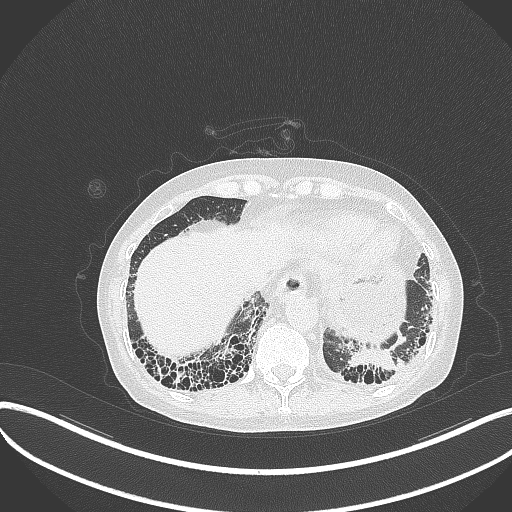
Chest CT, one axial slice. Position 58 of 373 along the scan axis. 120 kVp. Lung window (W 1500 / L -600 HU). 1 mm slice thickness. 512 × 512 image matrix, field of view 400 × 400 mm. Female patient, age 56 years. Case-level facts recorded for this patient, not image findings: clinical TNM (as recorded): T1 N0 M0.
Structures marked on this image (bounding box drawn by a radiologist):
- lung tumour (recorded histology: adenocarcinoma): box from (x=340, y=344) to (x=402, y=377) px